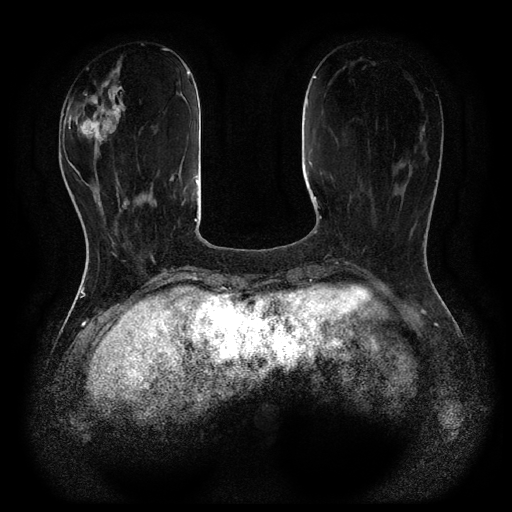
Breast MRI (dynamic contrast-enhanced, multi-phase), one axial slice; position 30 of 116 along the scan axis; dynamic contrast-enhanced series, time point 2 of 5 at this slice position (early post-contrast); 1.5 T; TE 2.6 ms, TR 5.4 ms; 512 × 512 image matrix. Patient: female, 48 years.
Structures marked on this image (semi-automatically segmented with operator editing):
- breast lesion (labelled benign in the annotation): box from (x=63, y=56) to (x=126, y=154) px